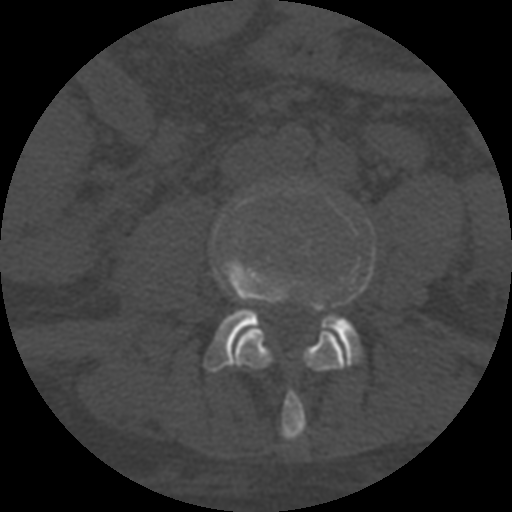
CT including the spine, one axial slice. Position 220 of 708 along the scan axis. Reconstruction kernel STANDARD. One of 3 acquisitions stored at this slice position. Bone window (W 1800 / L 400 HU). 512 × 512 image matrix, field of view 160 × 160 mm. Patient age 55 years. Case-level facts recorded for this patient, not image findings: primary cancer: colon; vertebrae with lytic lesions (as recorded): T12, L1, L5.
Annotated regions visible in this slice (semi-automatically segmented with operator editing):
- L3 vertebra: bounding box <233,328,348,441> (left, top, right, bottom; pixels)
- L4 vertebra: <203,199,375,372>